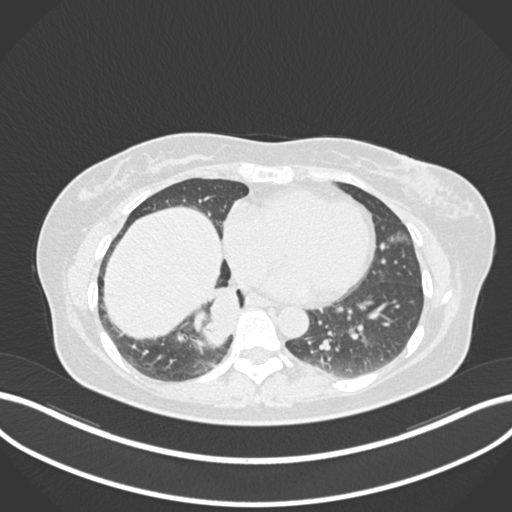
Chest CT, one axial slice. Lung window (W 1500 / L -600 HU). 512 × 512 image matrix, field of view 400 × 400 mm. Female patient, age 54 years. From the clinical record (not read from this slice): clinical TNM (as recorded): T4 N0 M0.
Structures marked on this image (bounding box drawn by a radiologist):
- lung tumour (recorded histology: adenocarcinoma): bounding box <196,284,242,352> (left, top, right, bottom; pixels)